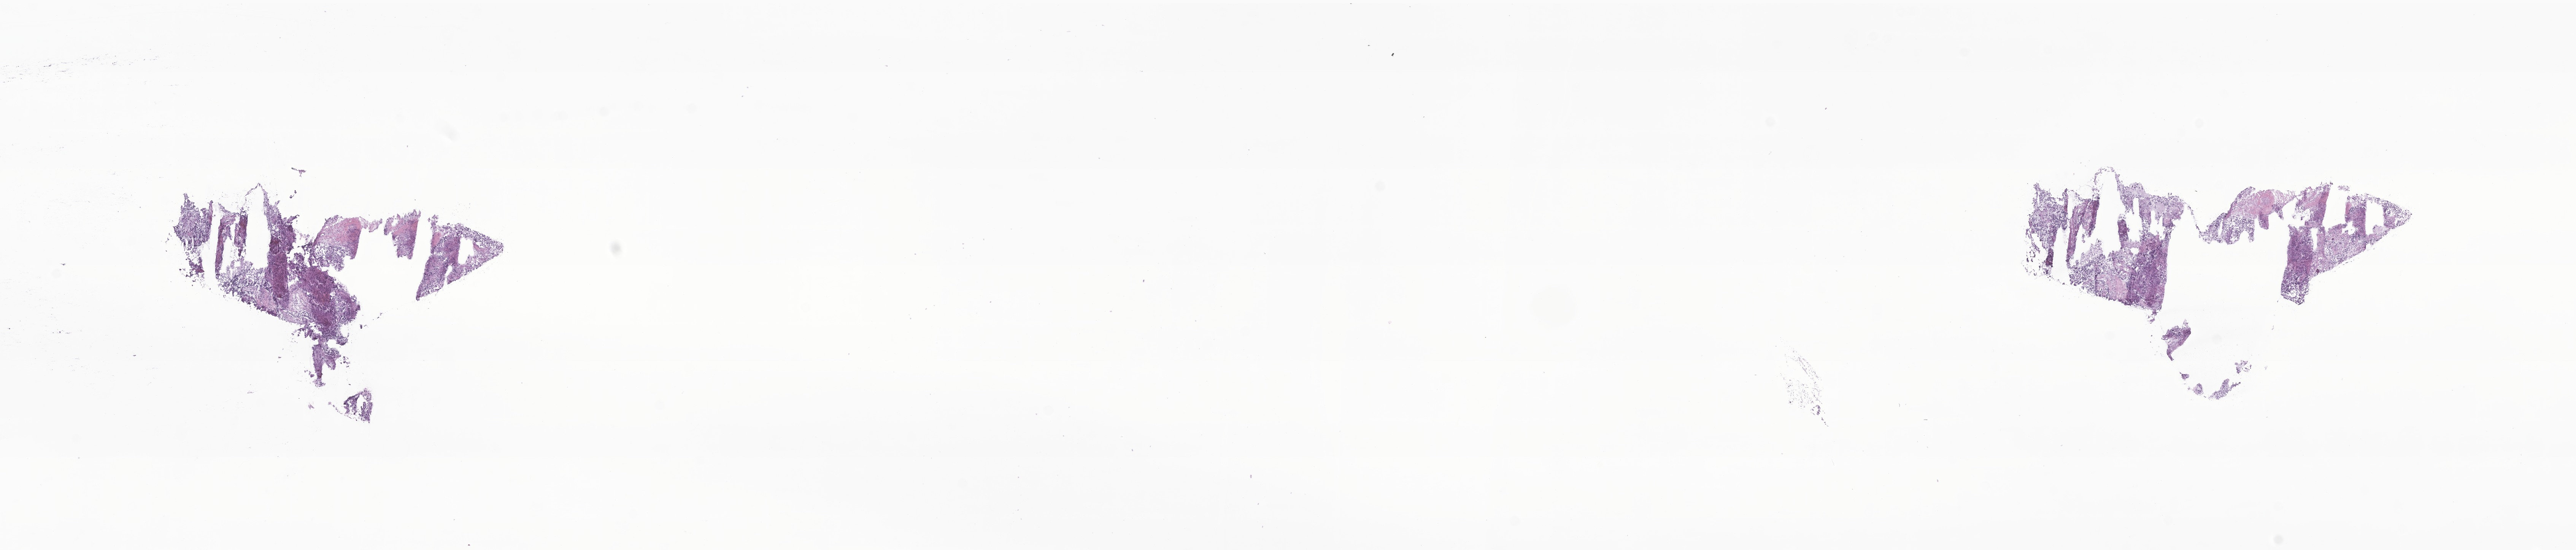
Digitized H&E-stained section of tumor tissue from the abdomen — shown as a low-resolution overview of the whole scanned area (about 28.6 x 6.1 mm). Frozen section. Patient: female, age 651 days (about 1.8 years).
* recorded diagnosis: Neoplasm, malignant